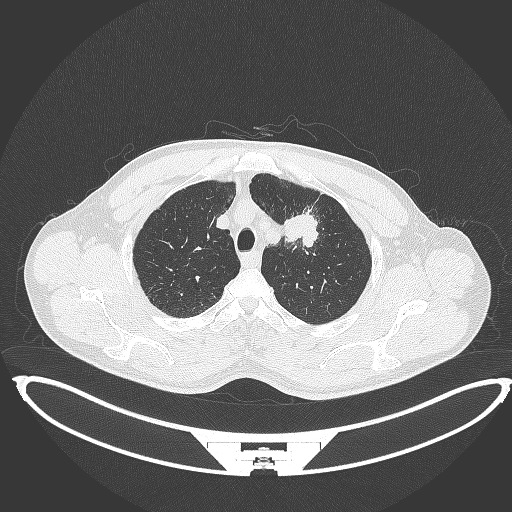
Chest CT, one axial slice. Slice 361 of 395 in the series (ordered by position). 120 kVp. Lung window (W 1500 / L -600 HU). 1 mm slice thickness. 512 × 512 image matrix. Male patient, age 60 years. From the clinical record (not read from this slice): clinical TNM (as recorded): T2a N0 M0.
Annotated regions visible in this slice (rectangle marked by the reading radiologist):
- lung tumour (recorded histology: squamous cell carcinoma): bounding box <280,211,319,248> (left, top, right, bottom; pixels)